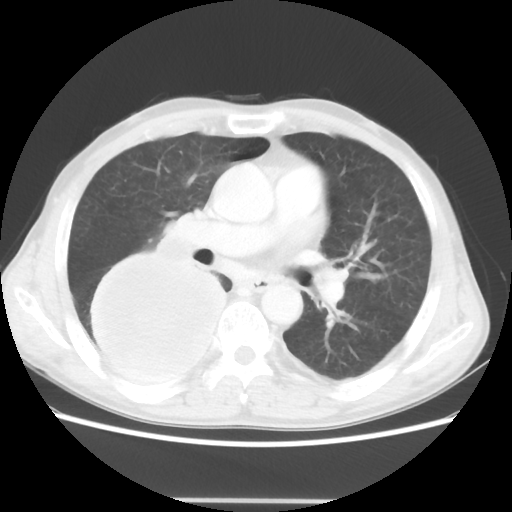
Chest CT, one axial slice; position 26 of 48 along the scan axis; lung window (W 1500 / L -600 HU); 5 mm slice thickness; 512 × 512 image matrix, field of view 361 × 361 mm. Male patient, age 66 years. From the clinical record (not read from this slice): clinical TNM (as recorded): T4 N1 M1; histopathological grade: G3.
Annotated regions visible in this slice (bounding box drawn by a radiologist):
- lung tumour (recorded histology: small cell carcinoma): bounding box [x1, y1, x2, y2] px = [80, 250, 235, 400]